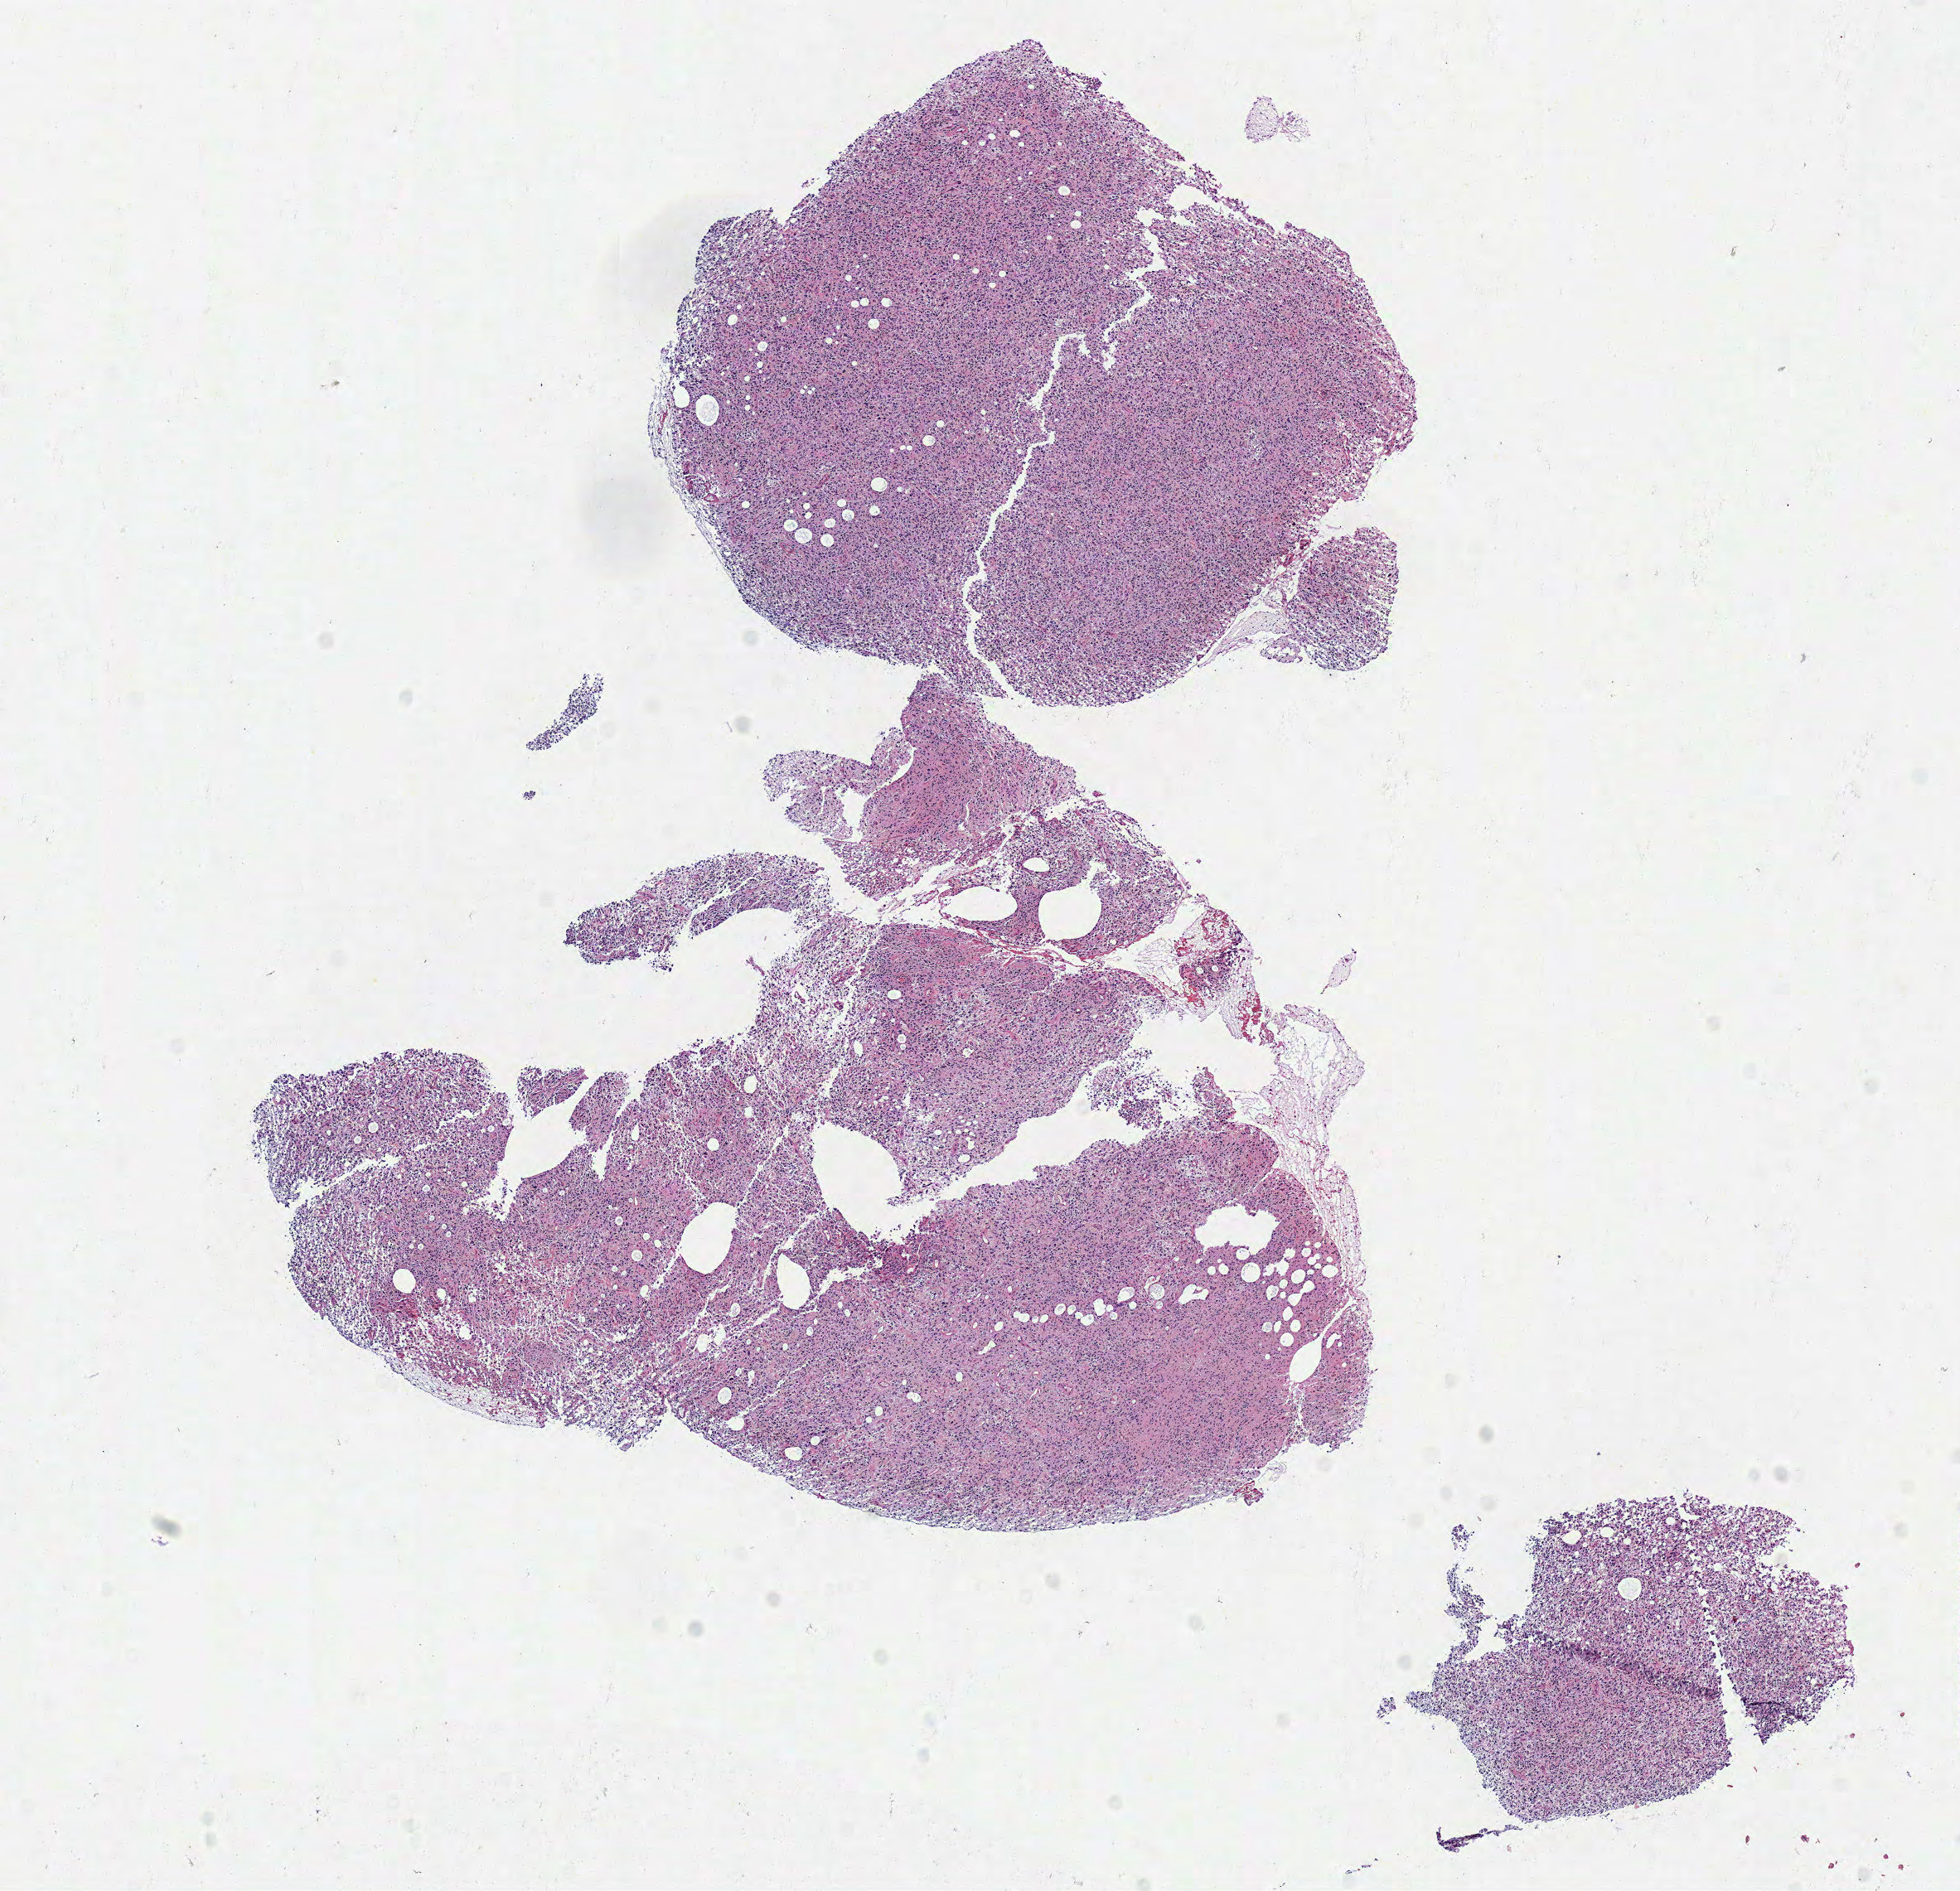
Whole-slide histology image, H&E — whole scanned area (about 9.3 x 9.0 mm, slide scanned at 40x) shown as a low-resolution overview, frozen section from the top of the tissue portion, primary tumour sample from the brain. Patient: male, age at initial diagnosis 52 years.
Histologic diagnosis: Astrocytoma, anaplastic (cerebrum).